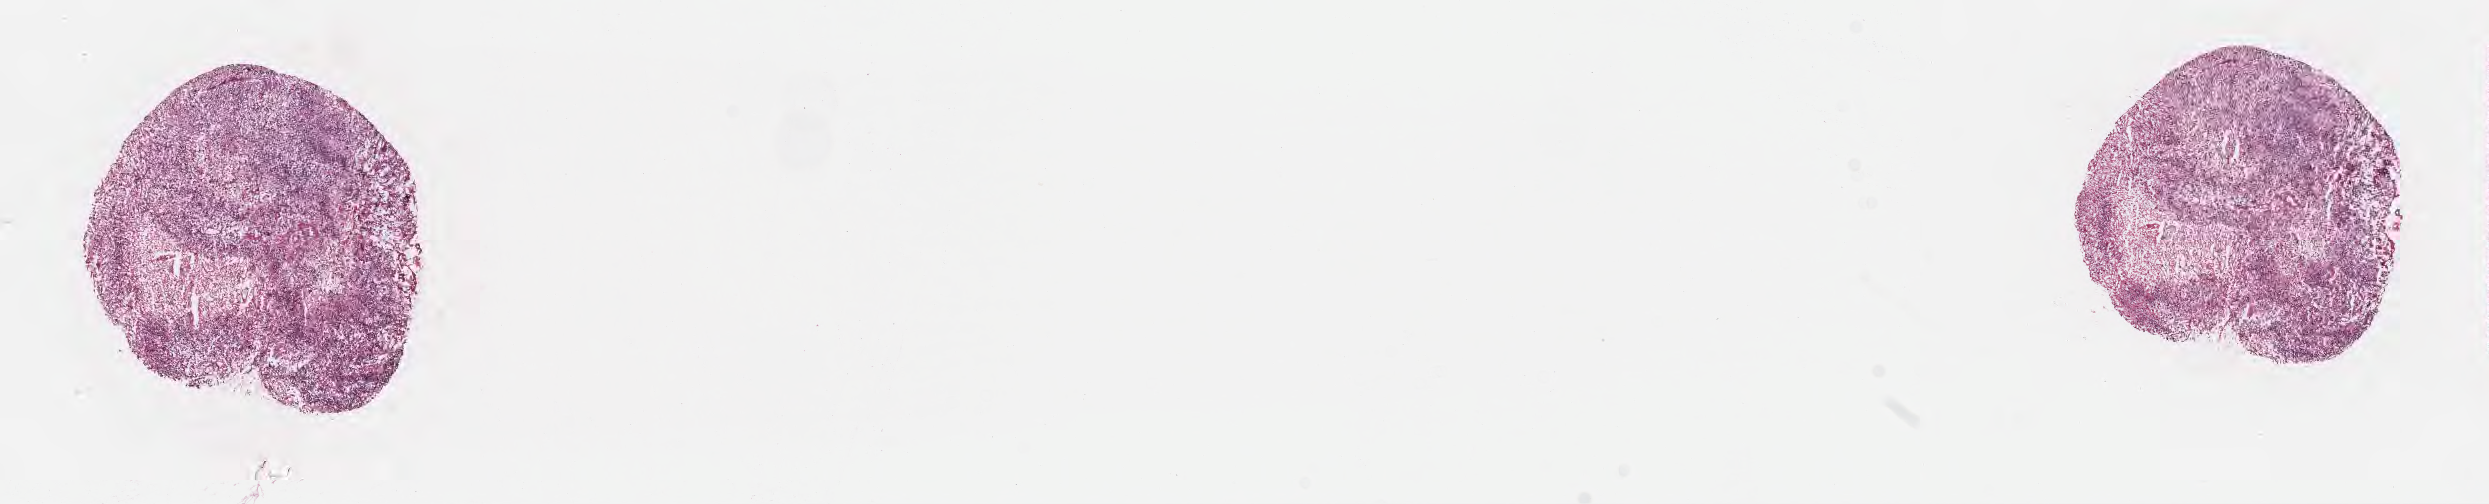
Digitized haematoxylin and eosin-stained section, low-resolution overview of the scanned area, about 20.1 x 4.1 mm. Cryosection. Primary tumor. Site: brain. Patient: male. Composition of this section per pathologist review: tumor cells 62%, tumor nuclei 91%, stromal cells 8%, necrosis 24%, normal cells 6%. Infiltration values recorded for this section: lymphocyte infiltration 0%, monocyte infiltration 0%, neutrophil infiltration 0%.
Section: bottom of the tissue portion. Diagnosis: Glioblastoma, NOS.